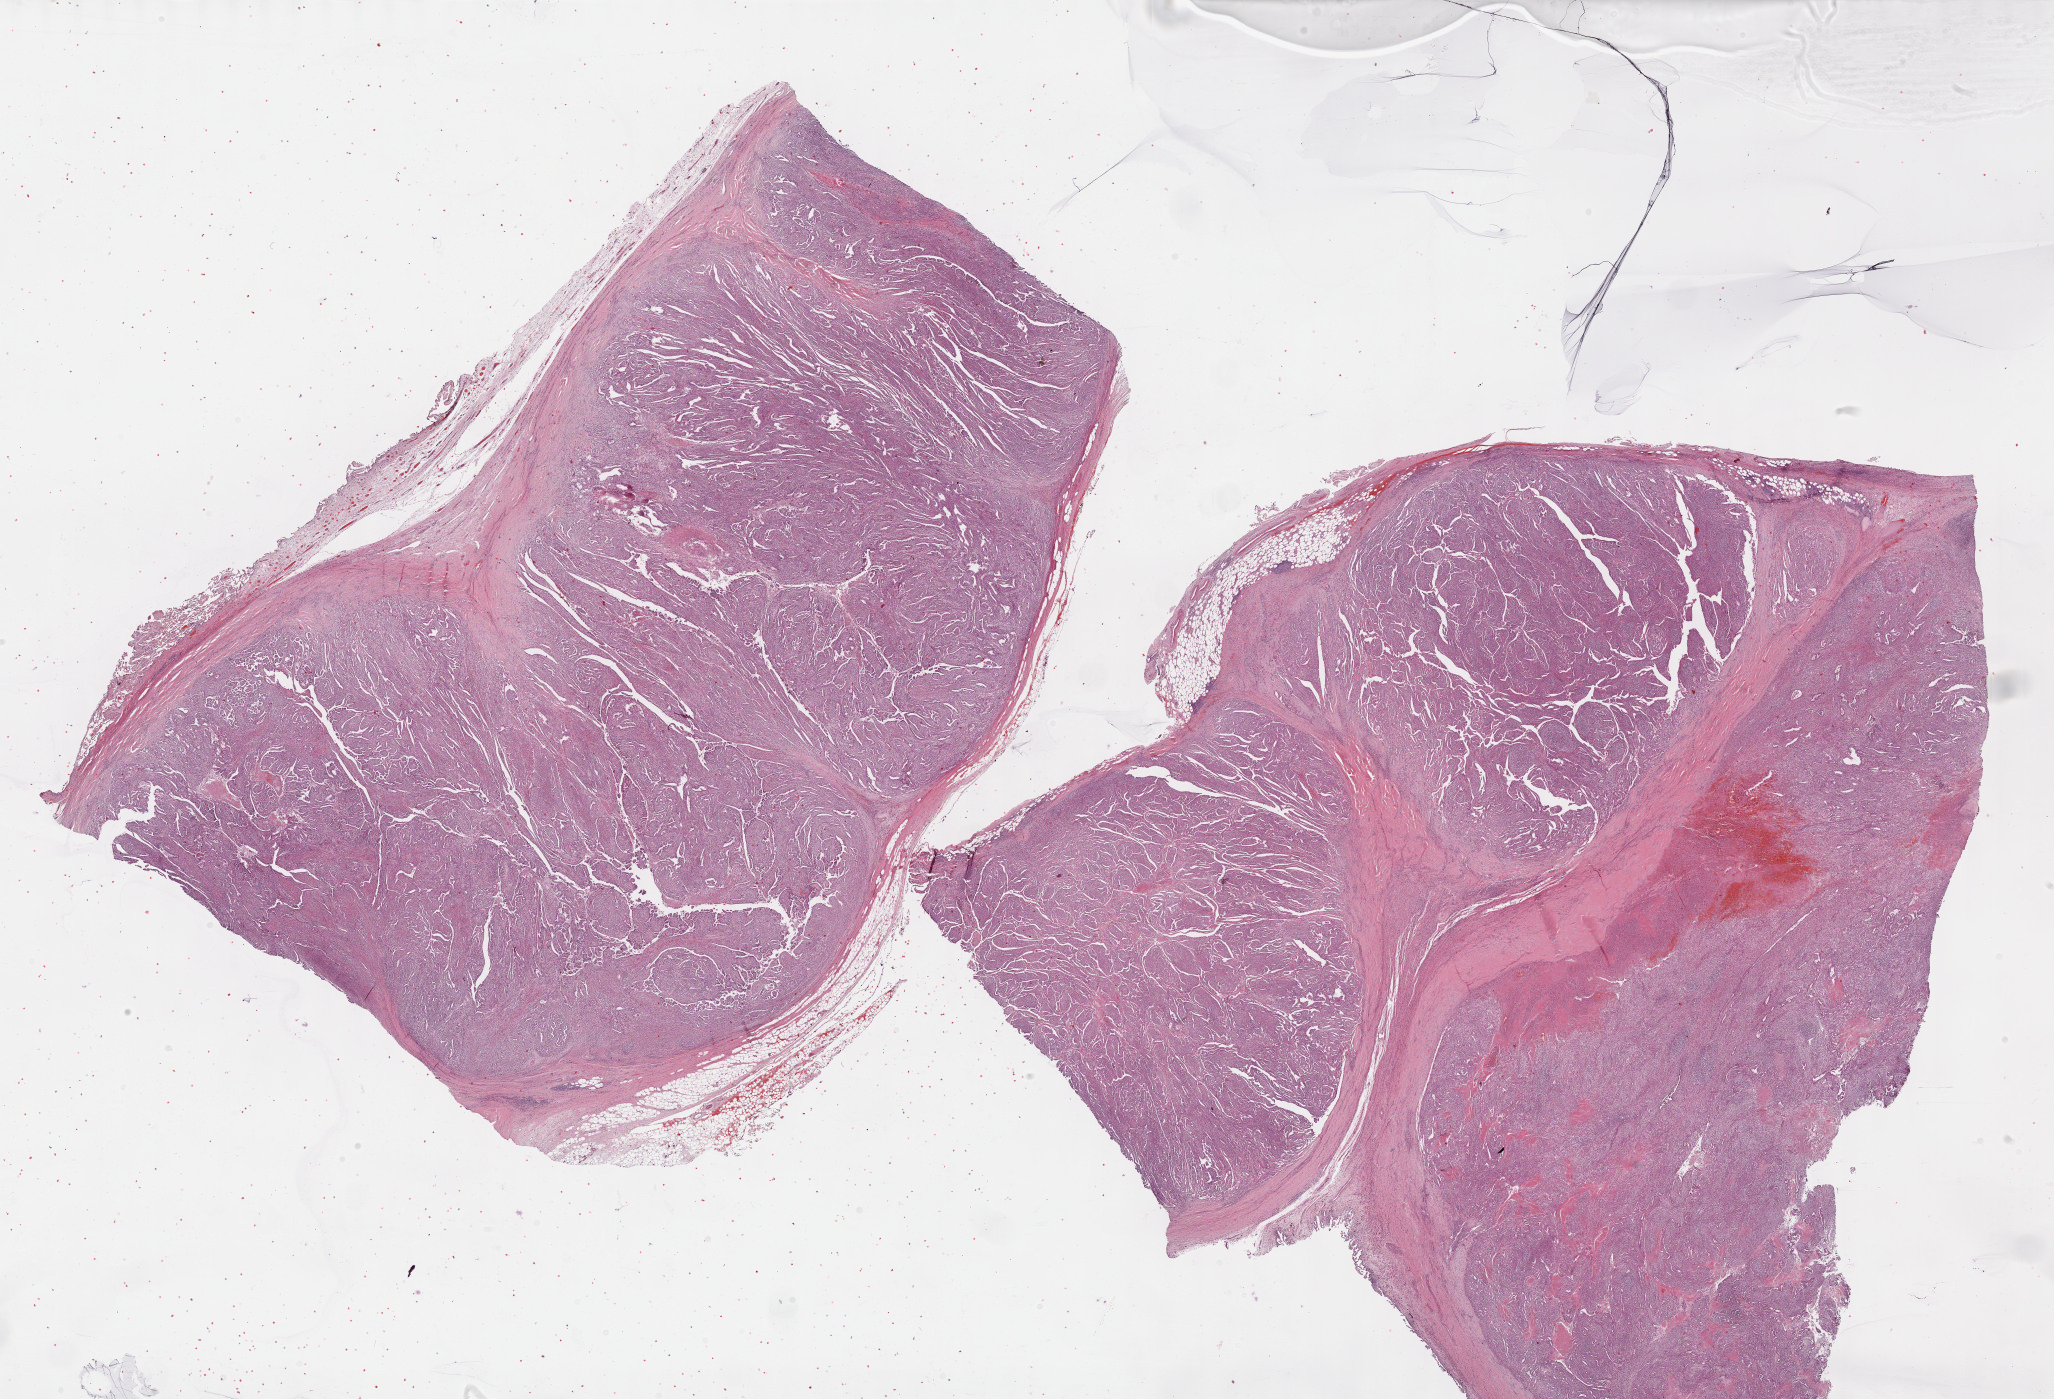
Hematoxylin and eosin (H&E) stained whole-slide image, shown as a low-resolution overview of the whole scanned area (about 33.2 x 22.6 mm, acquisition: 40x scan). Formalin-fixed paraffin-embedded (FFPE) diagnostic section. Sample: primary tumour, mesothelium. Male, age 67 years at initial diagnosis.
- pathologic diagnosis: Epithelioid mesothelioma, malignant (pleura, NOS)
- laterality: bilateral
- TNM: T3 N1 MX
- AJCC pathologic stage: III